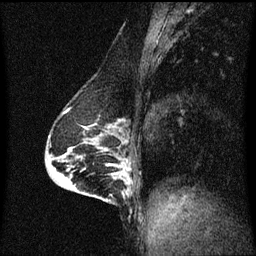
Breast MRI (dynamic contrast-enhanced), one sagittal slice. Slice 31 of 60 in the series (ordered by position). Dynamic contrast-enhanced series, image 2 of 3 at this slice position (ordered by acquisition). 1.5 T. TE 4.2 ms, TR 8.4 ms. 2 mm slice thickness. 256 × 256 image matrix. Patient: female, 64 years.
Annotated regions visible in this slice (semi-automatic segmentation, software-assisted and operator-edited):
- analysis volume of interest (the breast-tissue region the enhancement analysis was run in; not a lesion): bounding box <90,164,129,203> (left, top, right, bottom; pixels)
- tumour enhancement mask (voxels above the 70 % enhancement threshold inside the analysis volume of interest): <108,164,129,195>